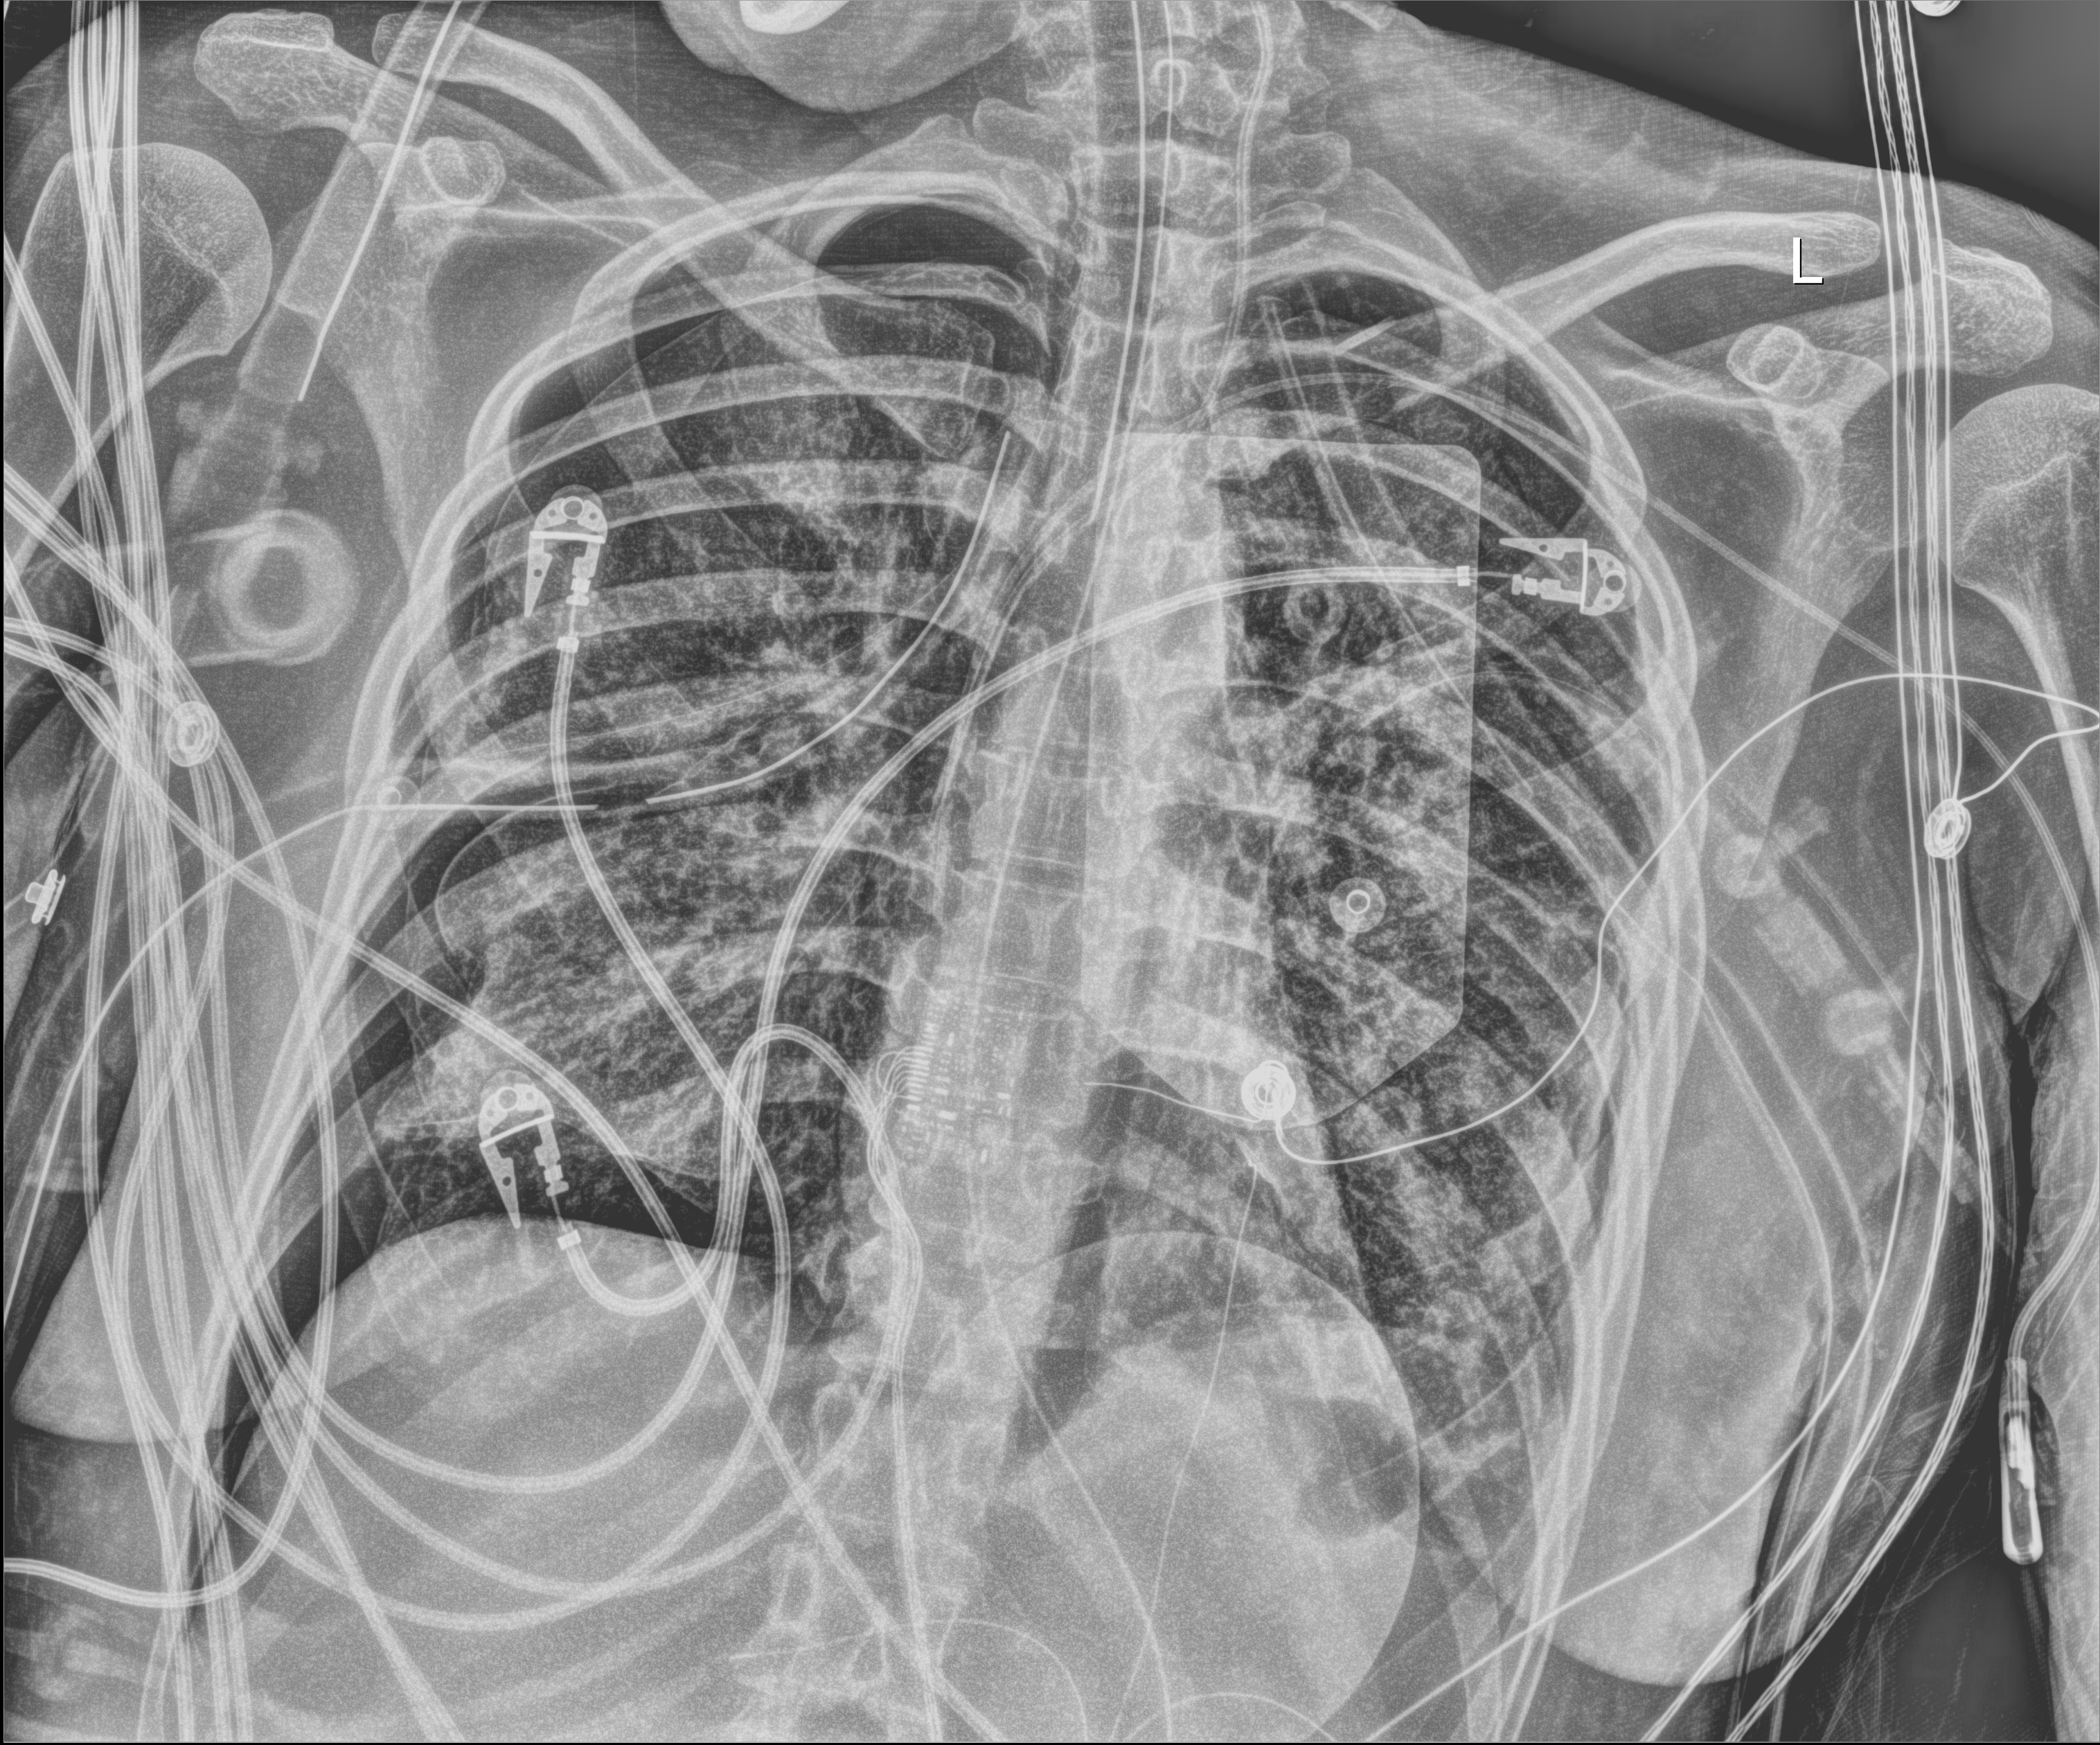
Chest X-ray (portable). Patient hospitalised with COVID-19, aged 18–59 years.
From the hospital-stay record, not from the radiograph (when in the stay this image was taken is not recorded): other chronic lung disease (admission record): no; COPD (admission record): no; mechanically ventilated during this hospital stay: yes.